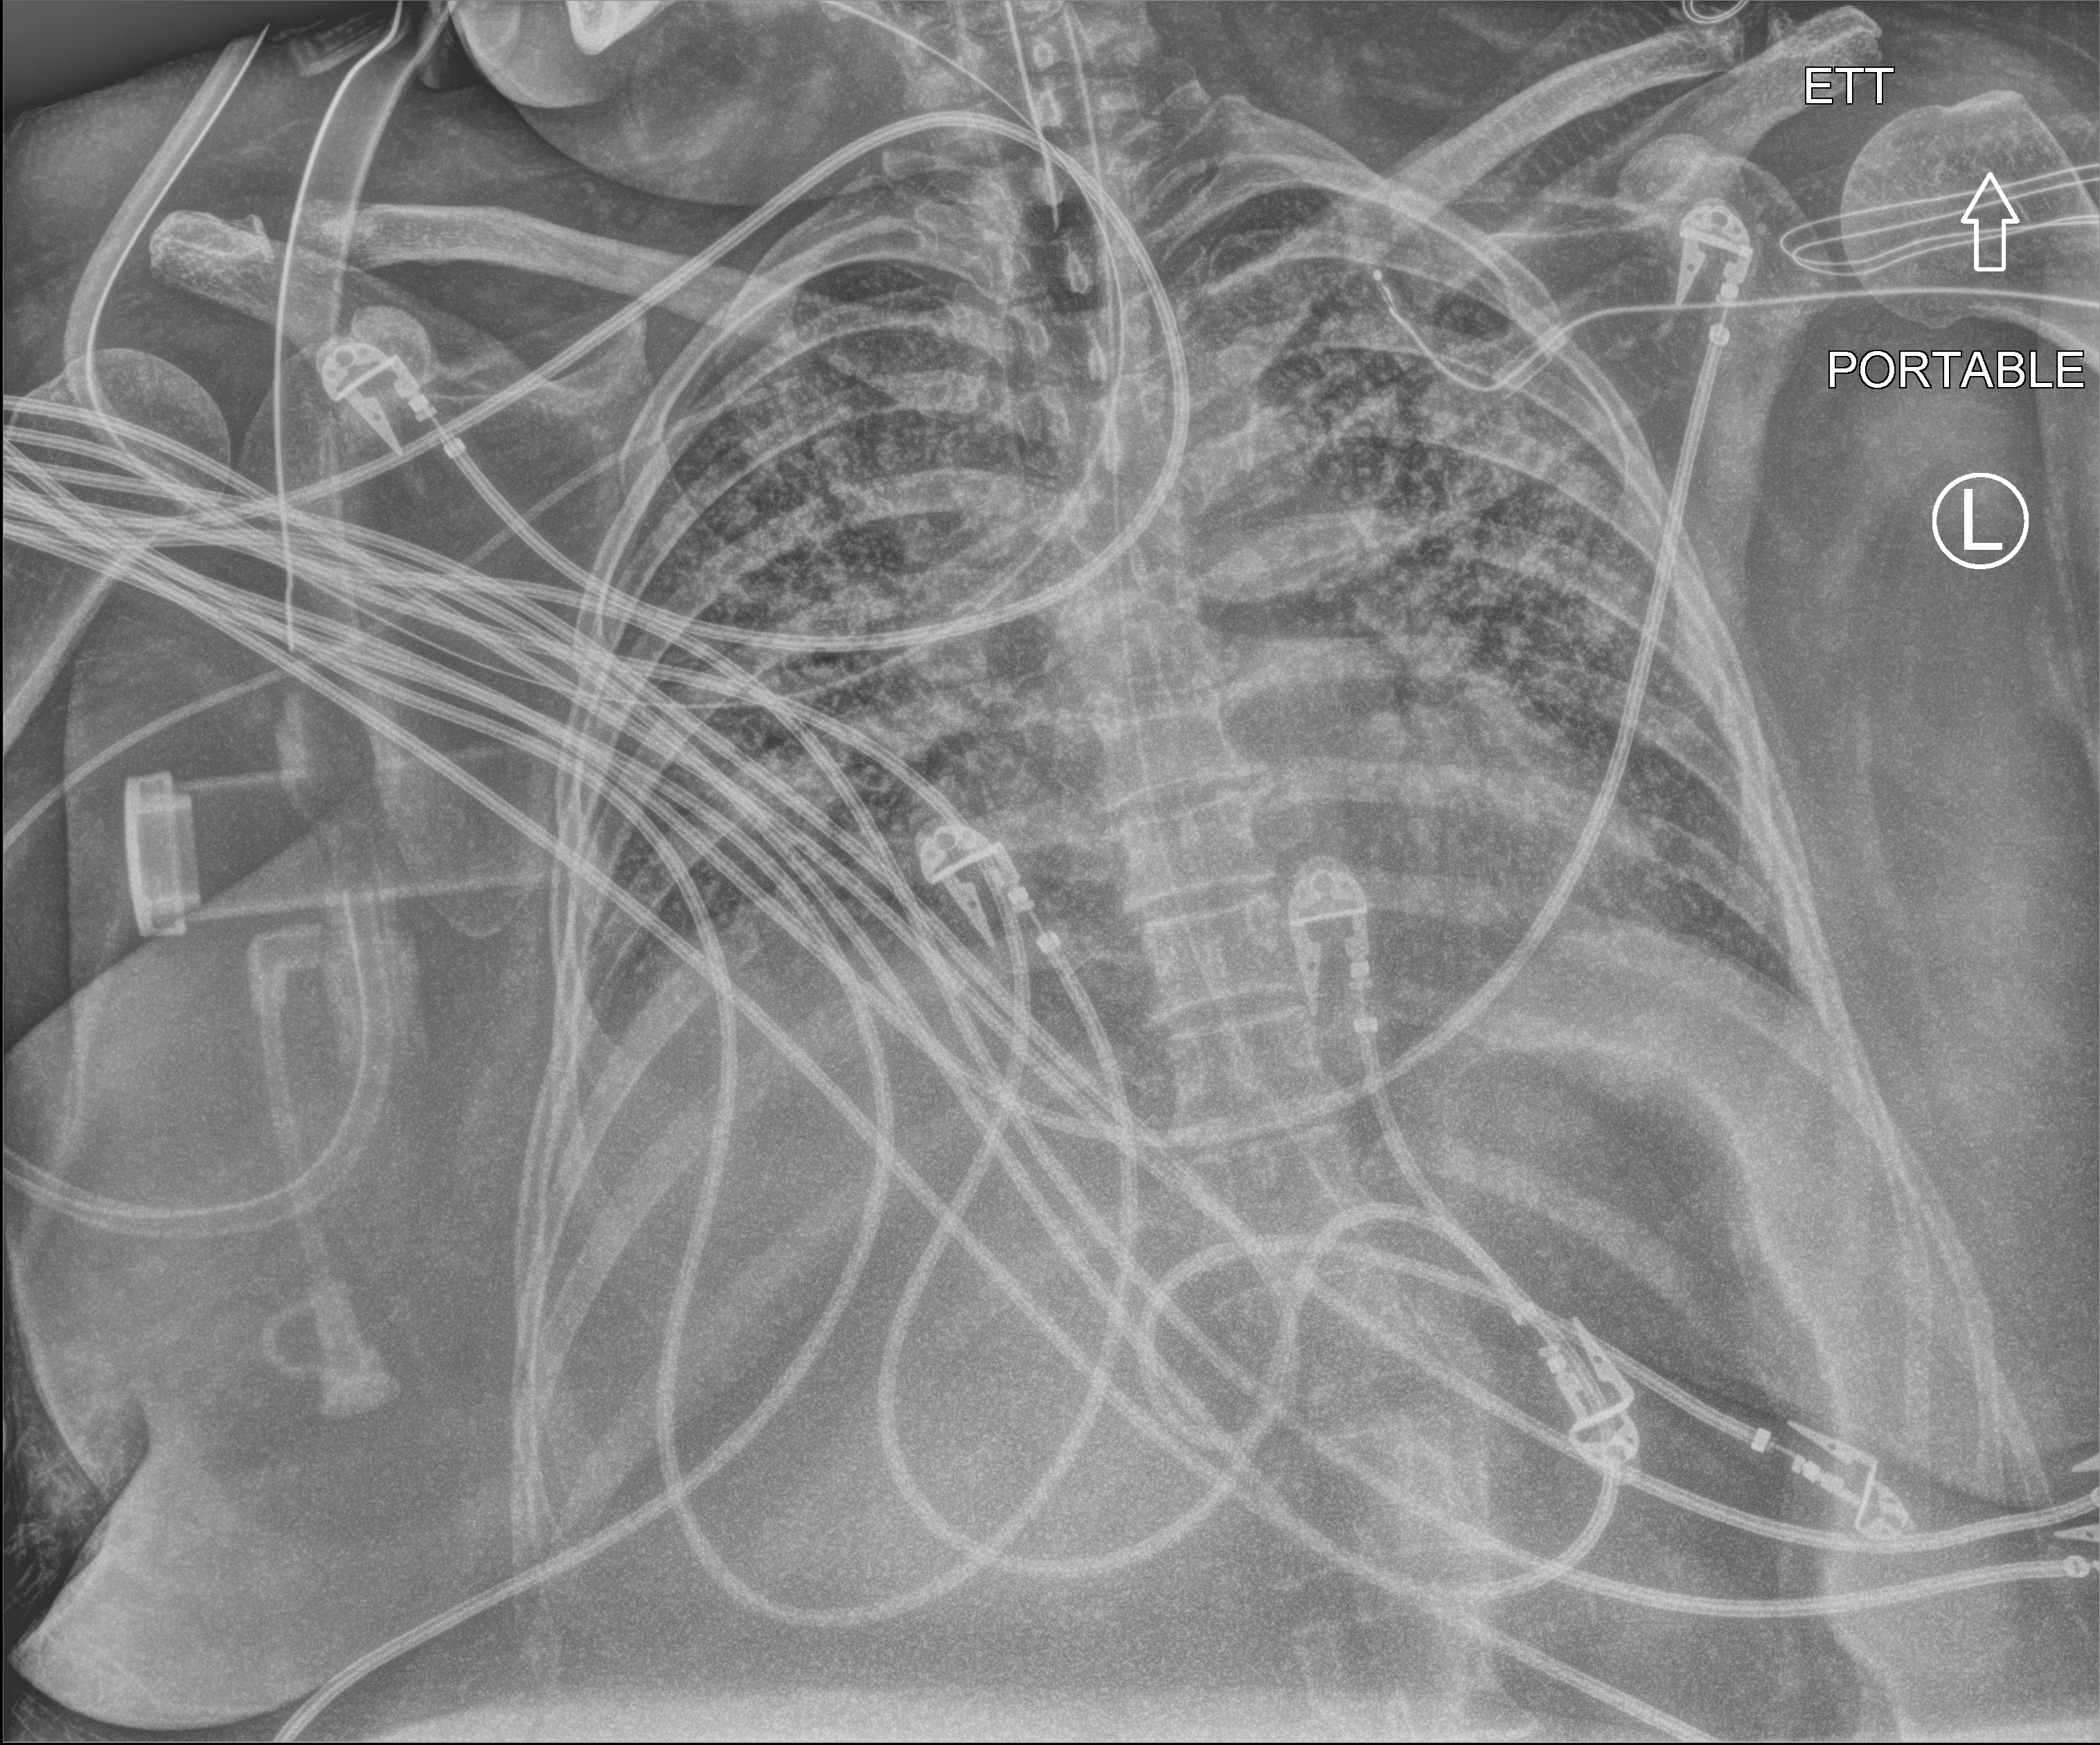
Chest X-ray (portable). Patient hospitalised with COVID-19; female, aged 18–59 years.
Hospital-stay facts (about this admission, not read from this image; timing relative to this image not recorded):
- mechanically ventilated during this hospital stay: yes